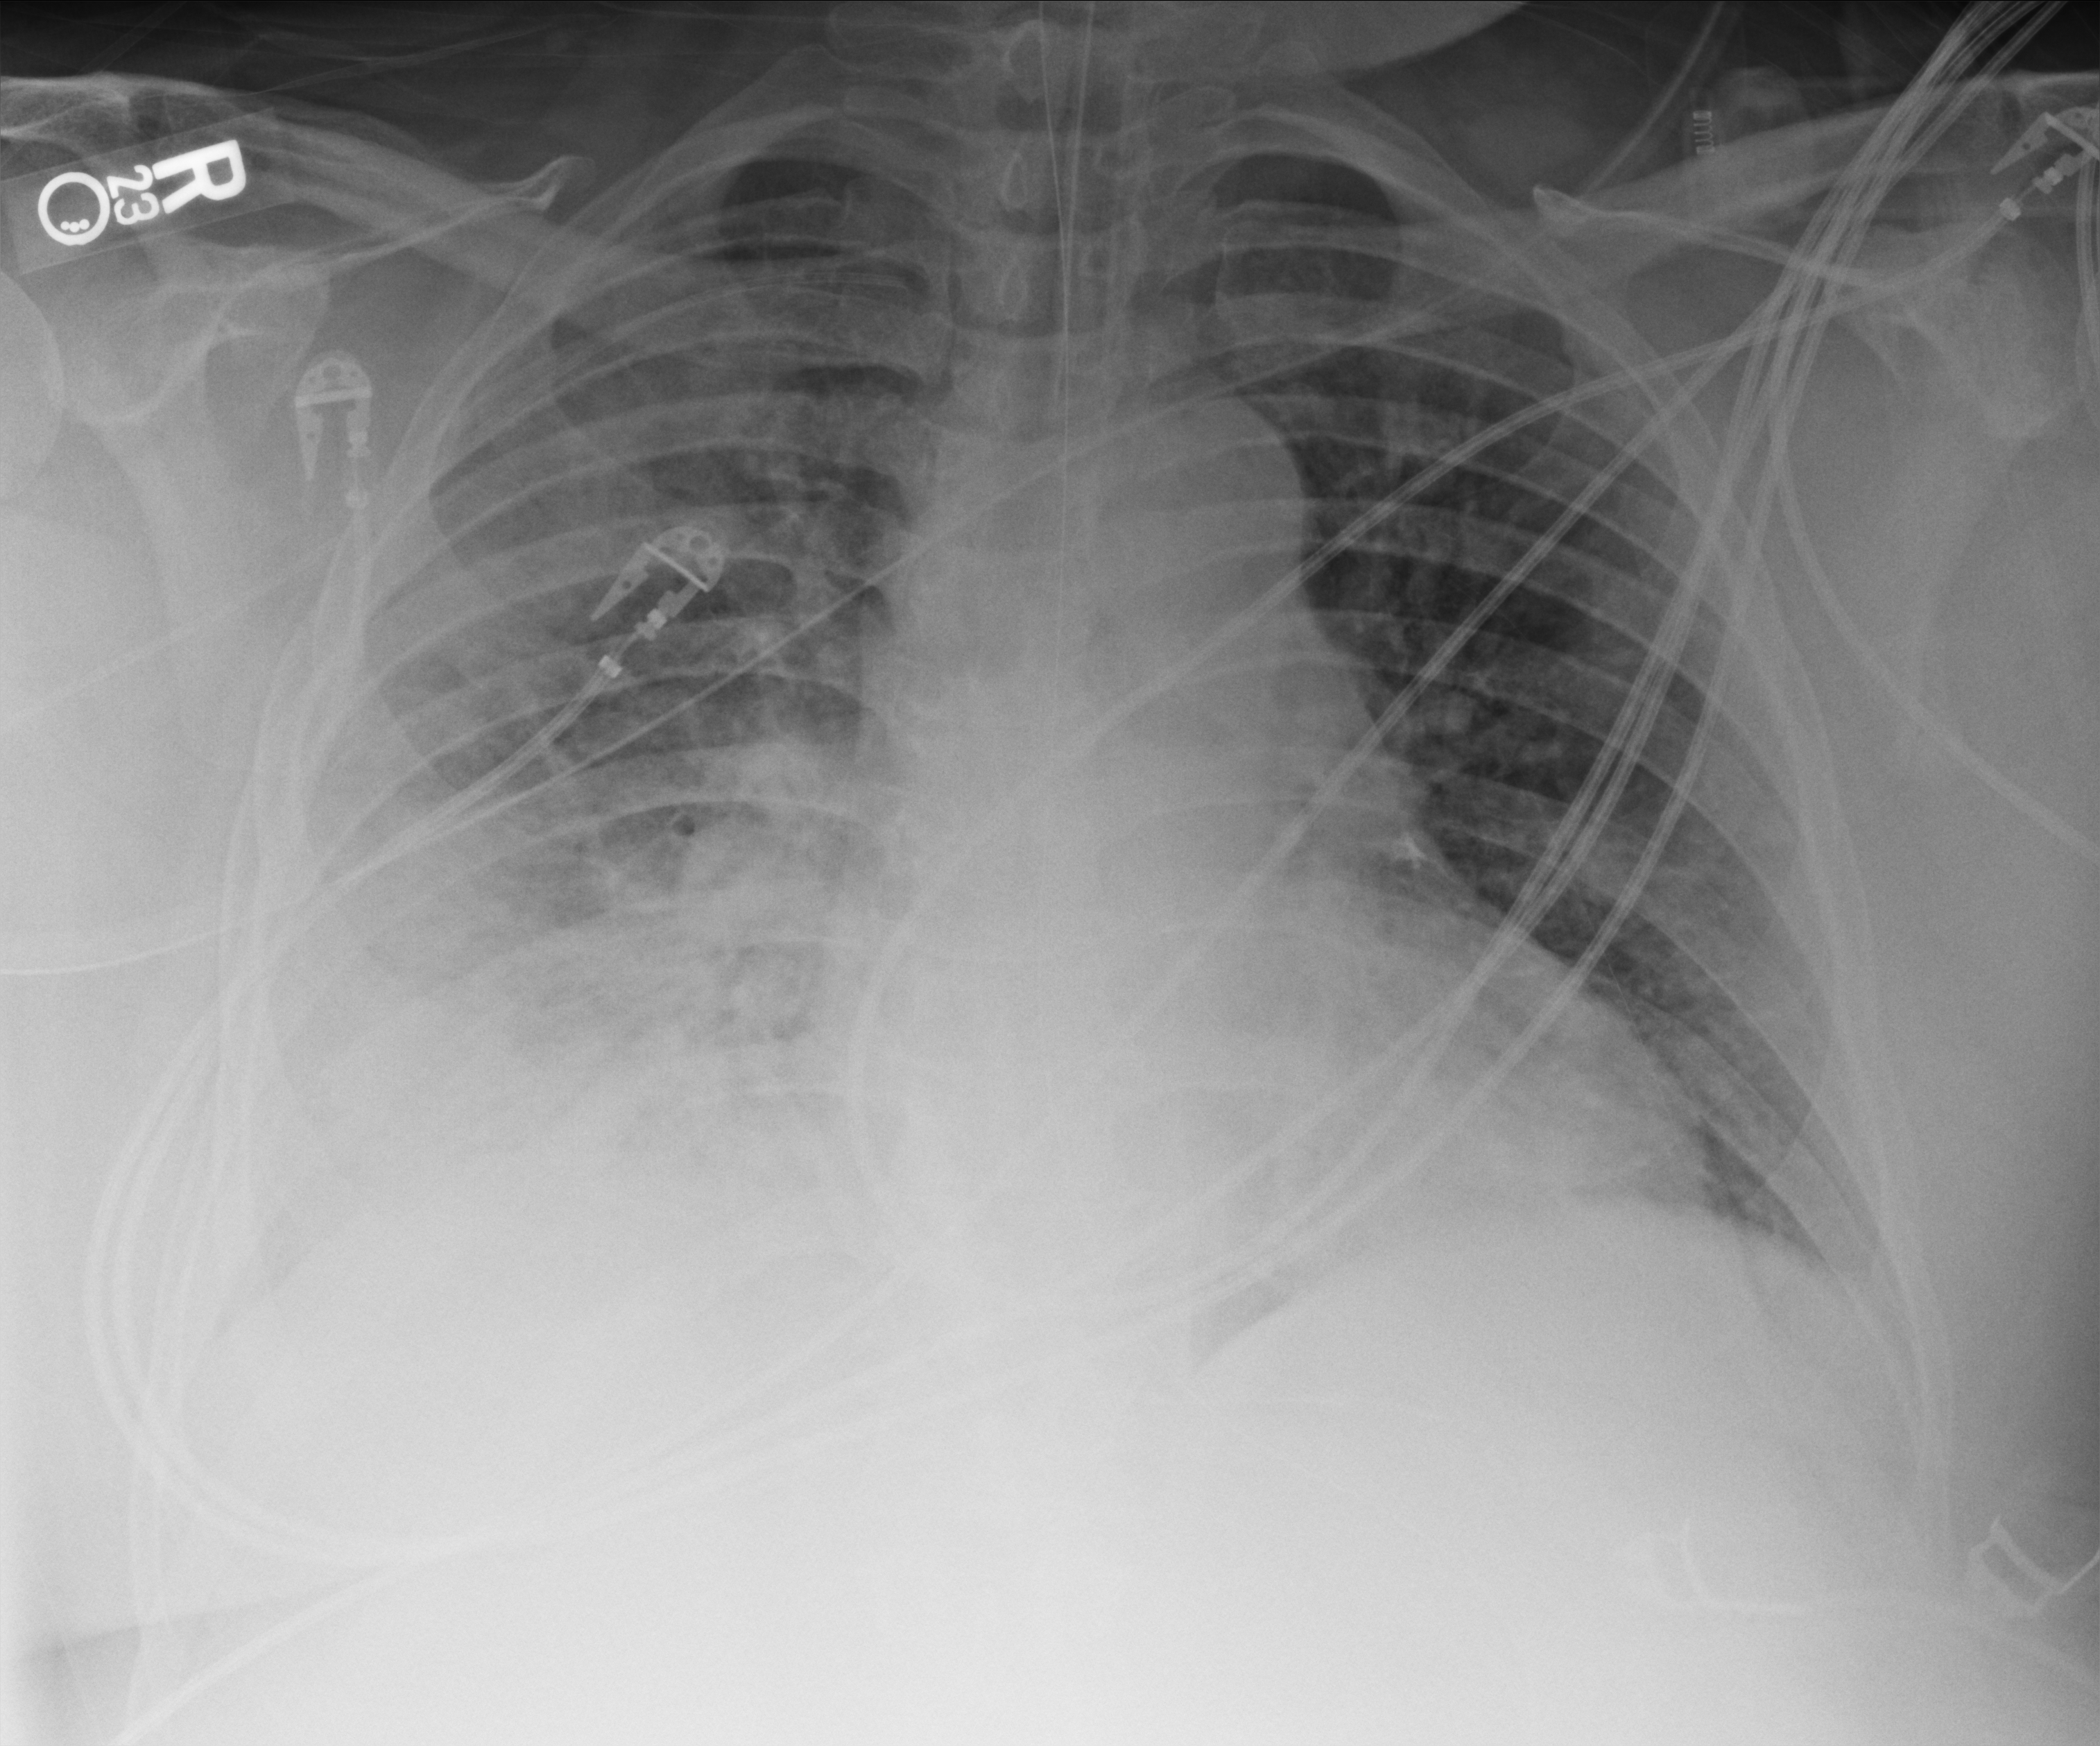
Portable chest radiograph, anteroposterior (AP) projection. Male patient hospitalised with COVID-19, age 18–59 years.
From the hospital-stay record, not from the radiograph (when in the stay this image was taken is not recorded): admitted to intensive care during this hospital stay: yes; smoking status (admission record): never.